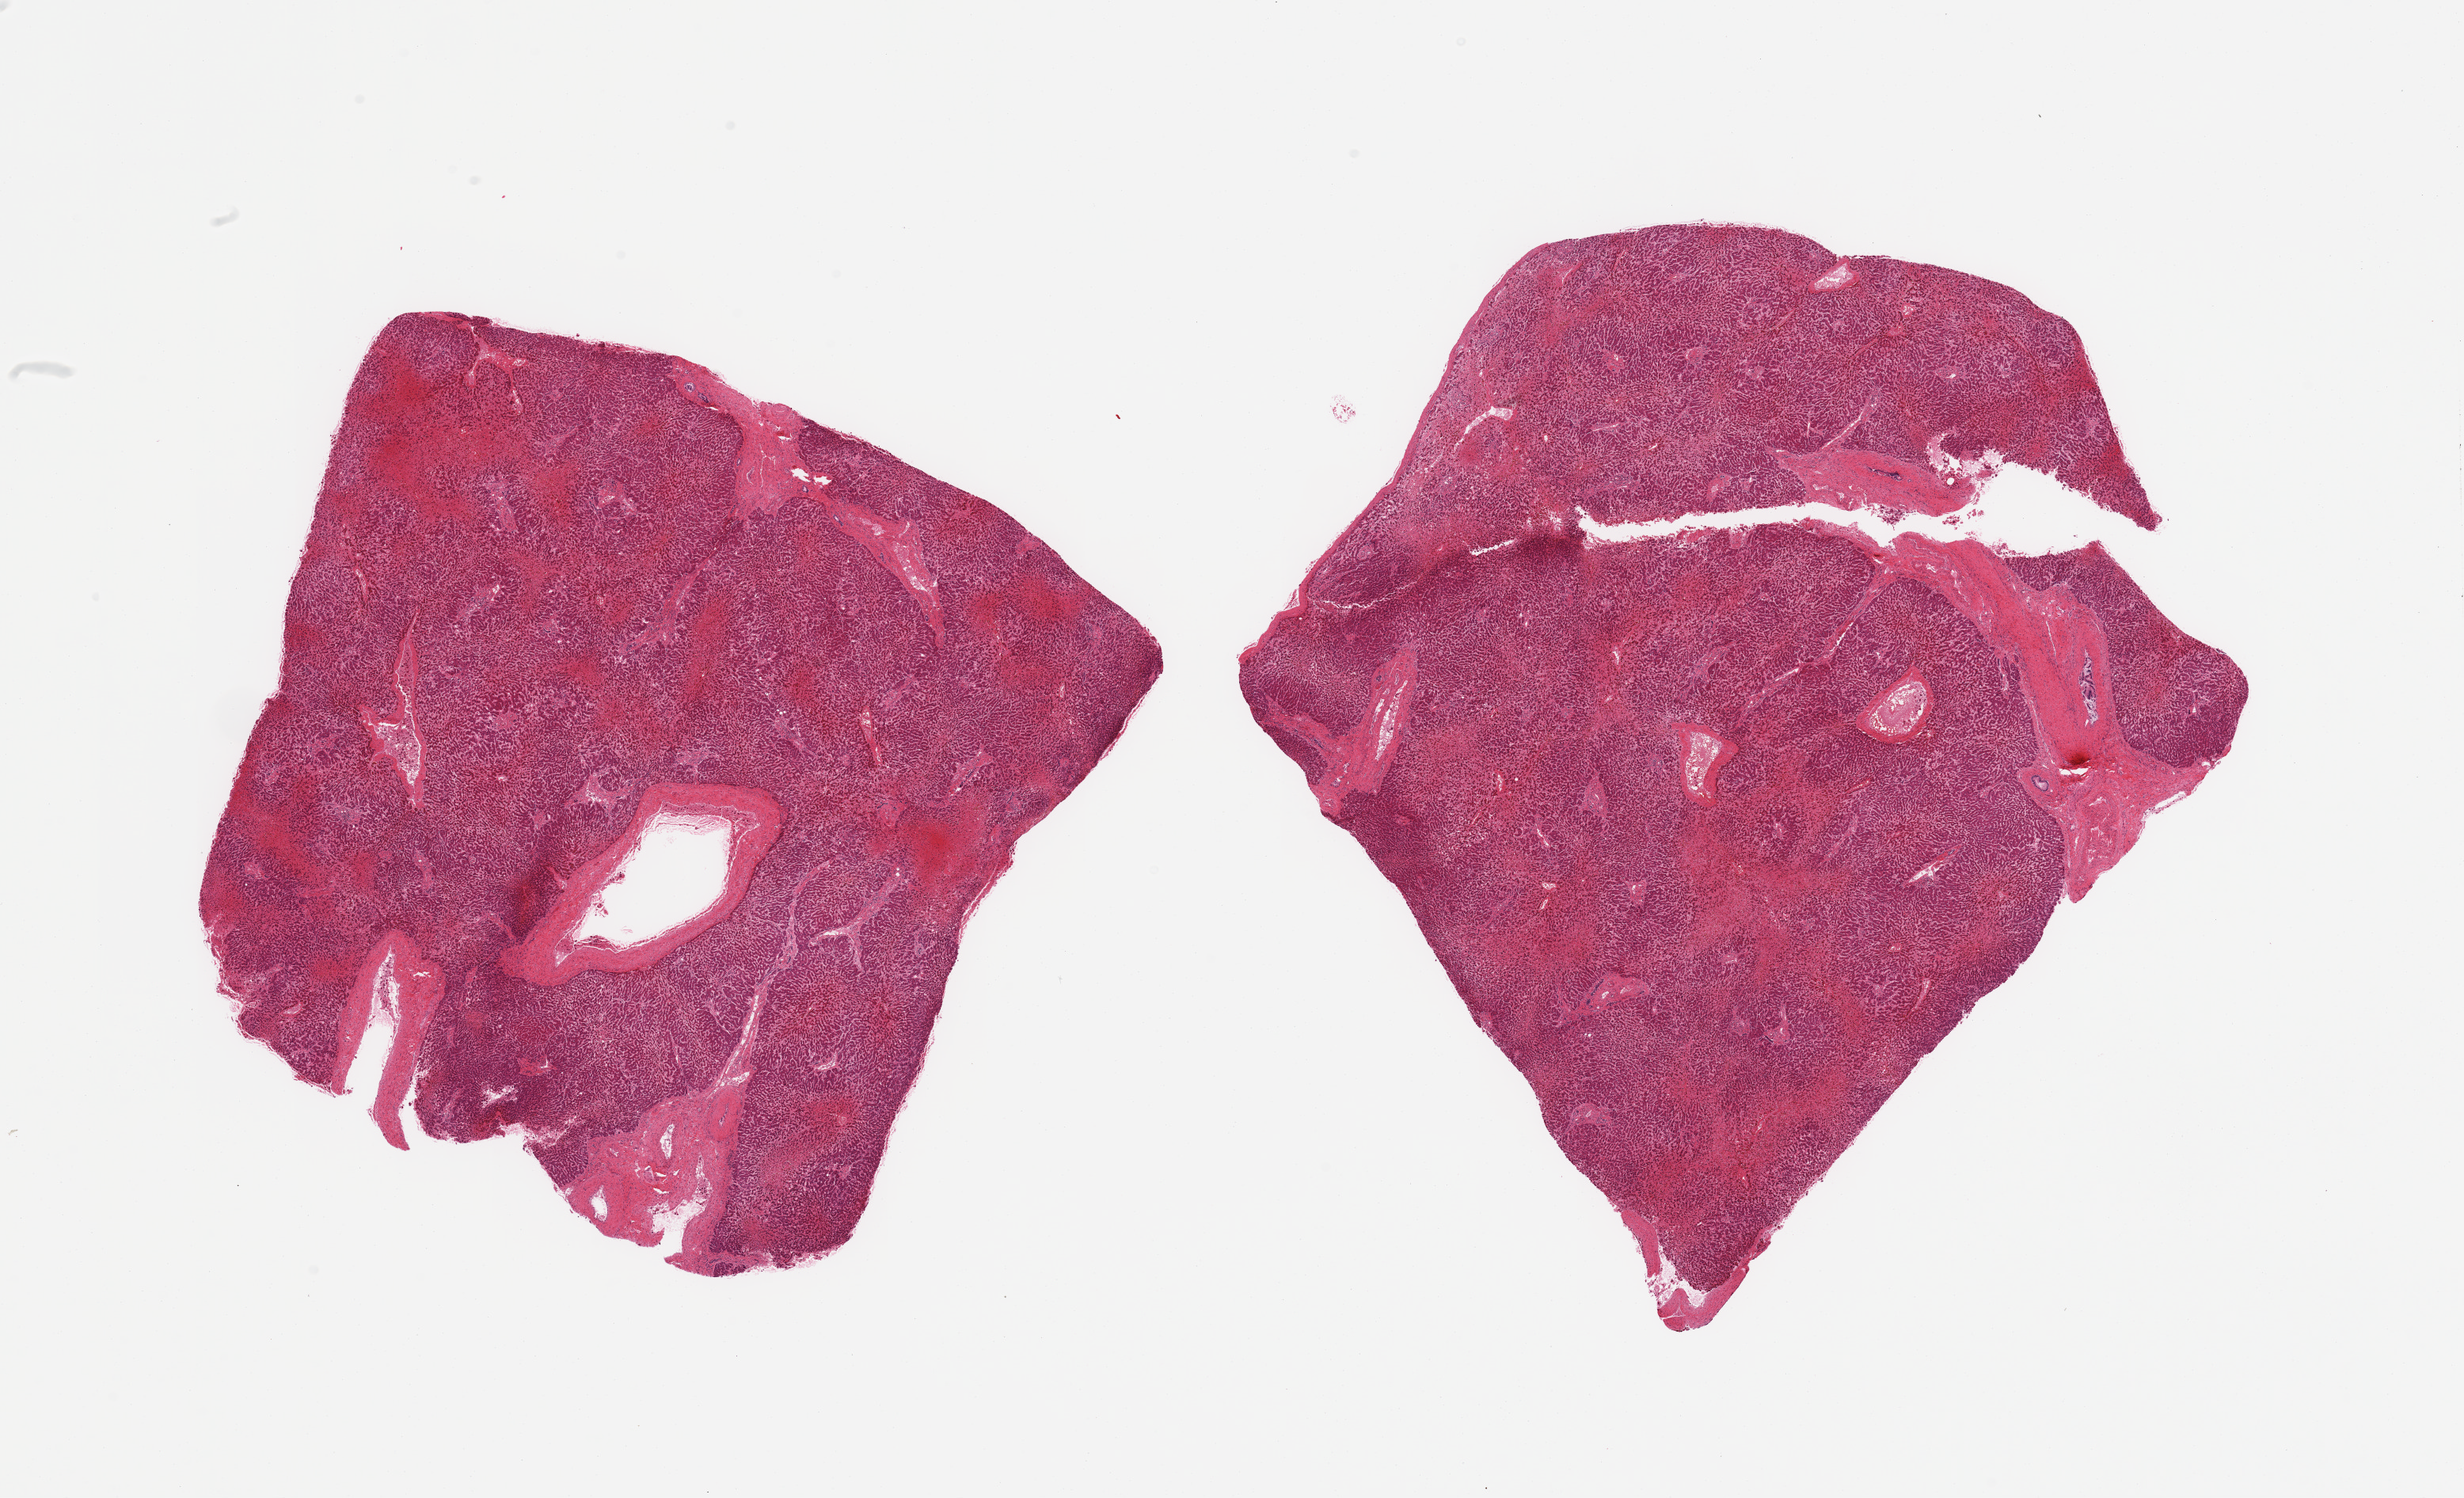
Digitized hematoxylin and eosin (H&E)-stained section — shown as a low-resolution overview of the whole scanned area (about 24.6 x 15.0 mm, from a 20x scan). PAXgene-fixed, paraffin-embedded tissue. Target tissue: liver. Tissue donor sample. Donor: male.
Pathologist's review note for this sample: 2 pieces; moderate central congestion and cord cell degeneration.